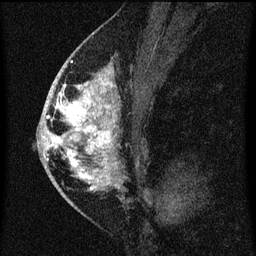
Breast MRI (dynamic contrast-enhanced), one sagittal slice; dynamic contrast-enhanced series, image 2 of 3 at this slice position (ordered by acquisition); 1.5 T; TE 4.2 ms, TR 8 ms; 2 mm slice thickness; 256 × 256 image matrix, field of view 180 × 180 mm. Female patient, age 46 years.
Annotated regions visible in this slice (semi-automatic segmentation, software-assisted and operator-edited):
- analysis volume of interest (the breast-tissue region the enhancement analysis was run in; not a lesion): bounding box <48,68,119,195> (left, top, right, bottom; pixels)
- tumour enhancement mask (voxels above the 70 % enhancement threshold inside the analysis volume of interest): <48,68,119,191>